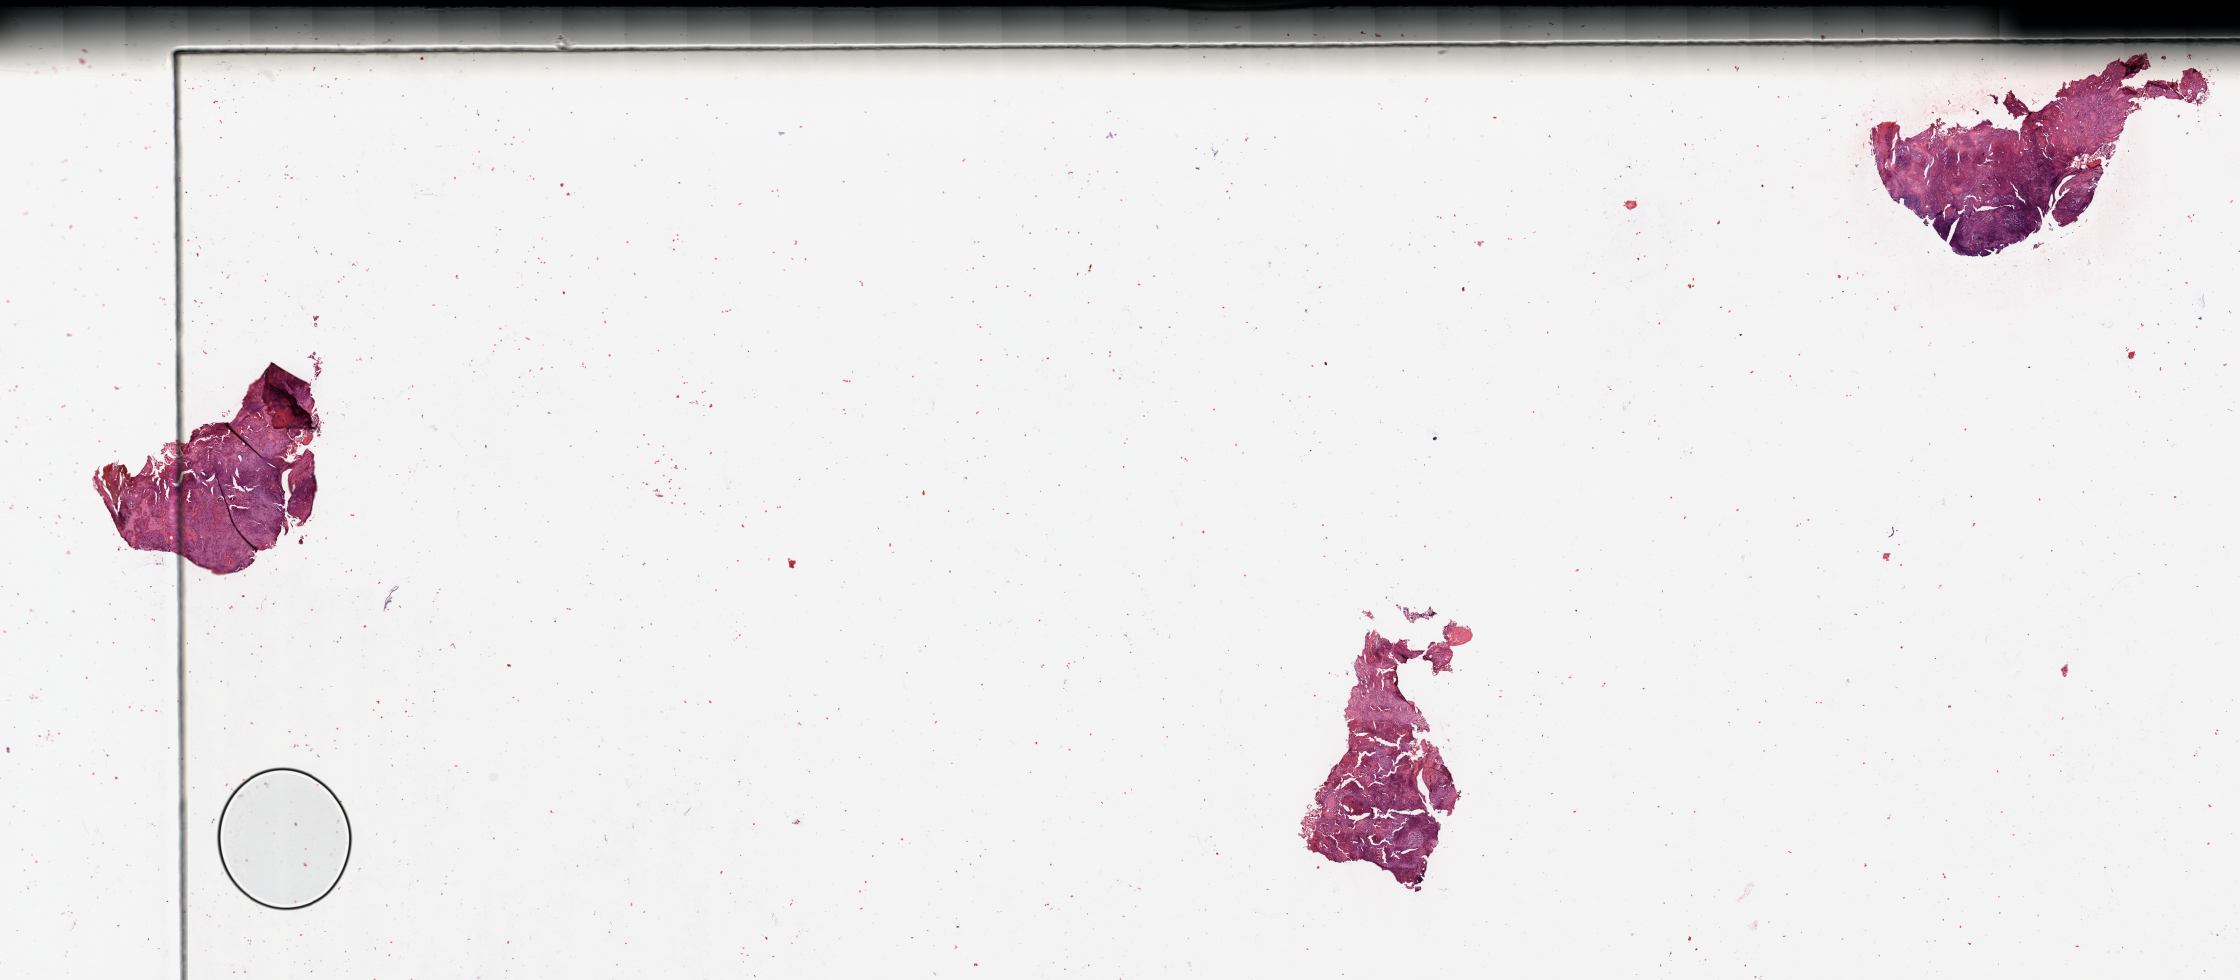
H&E-stained whole-slide image, low-resolution overview of the scanned area, about 35.4 x 15.5 mm (from a 20x scan), tumour tissue sample, sampled site: larynx. Patient: male, age 59 years. Histologic grade: G2 (moderately differentiated). Pathologist review of this section (percent, as recorded): tumour nuclei 85%, necrosis 5%.
Histologic diagnosis: Squamous cell carcinoma, NOS (larynx, NOS). AJCC pathologic stage: III. Primary tumour site (as recorded): larynx.